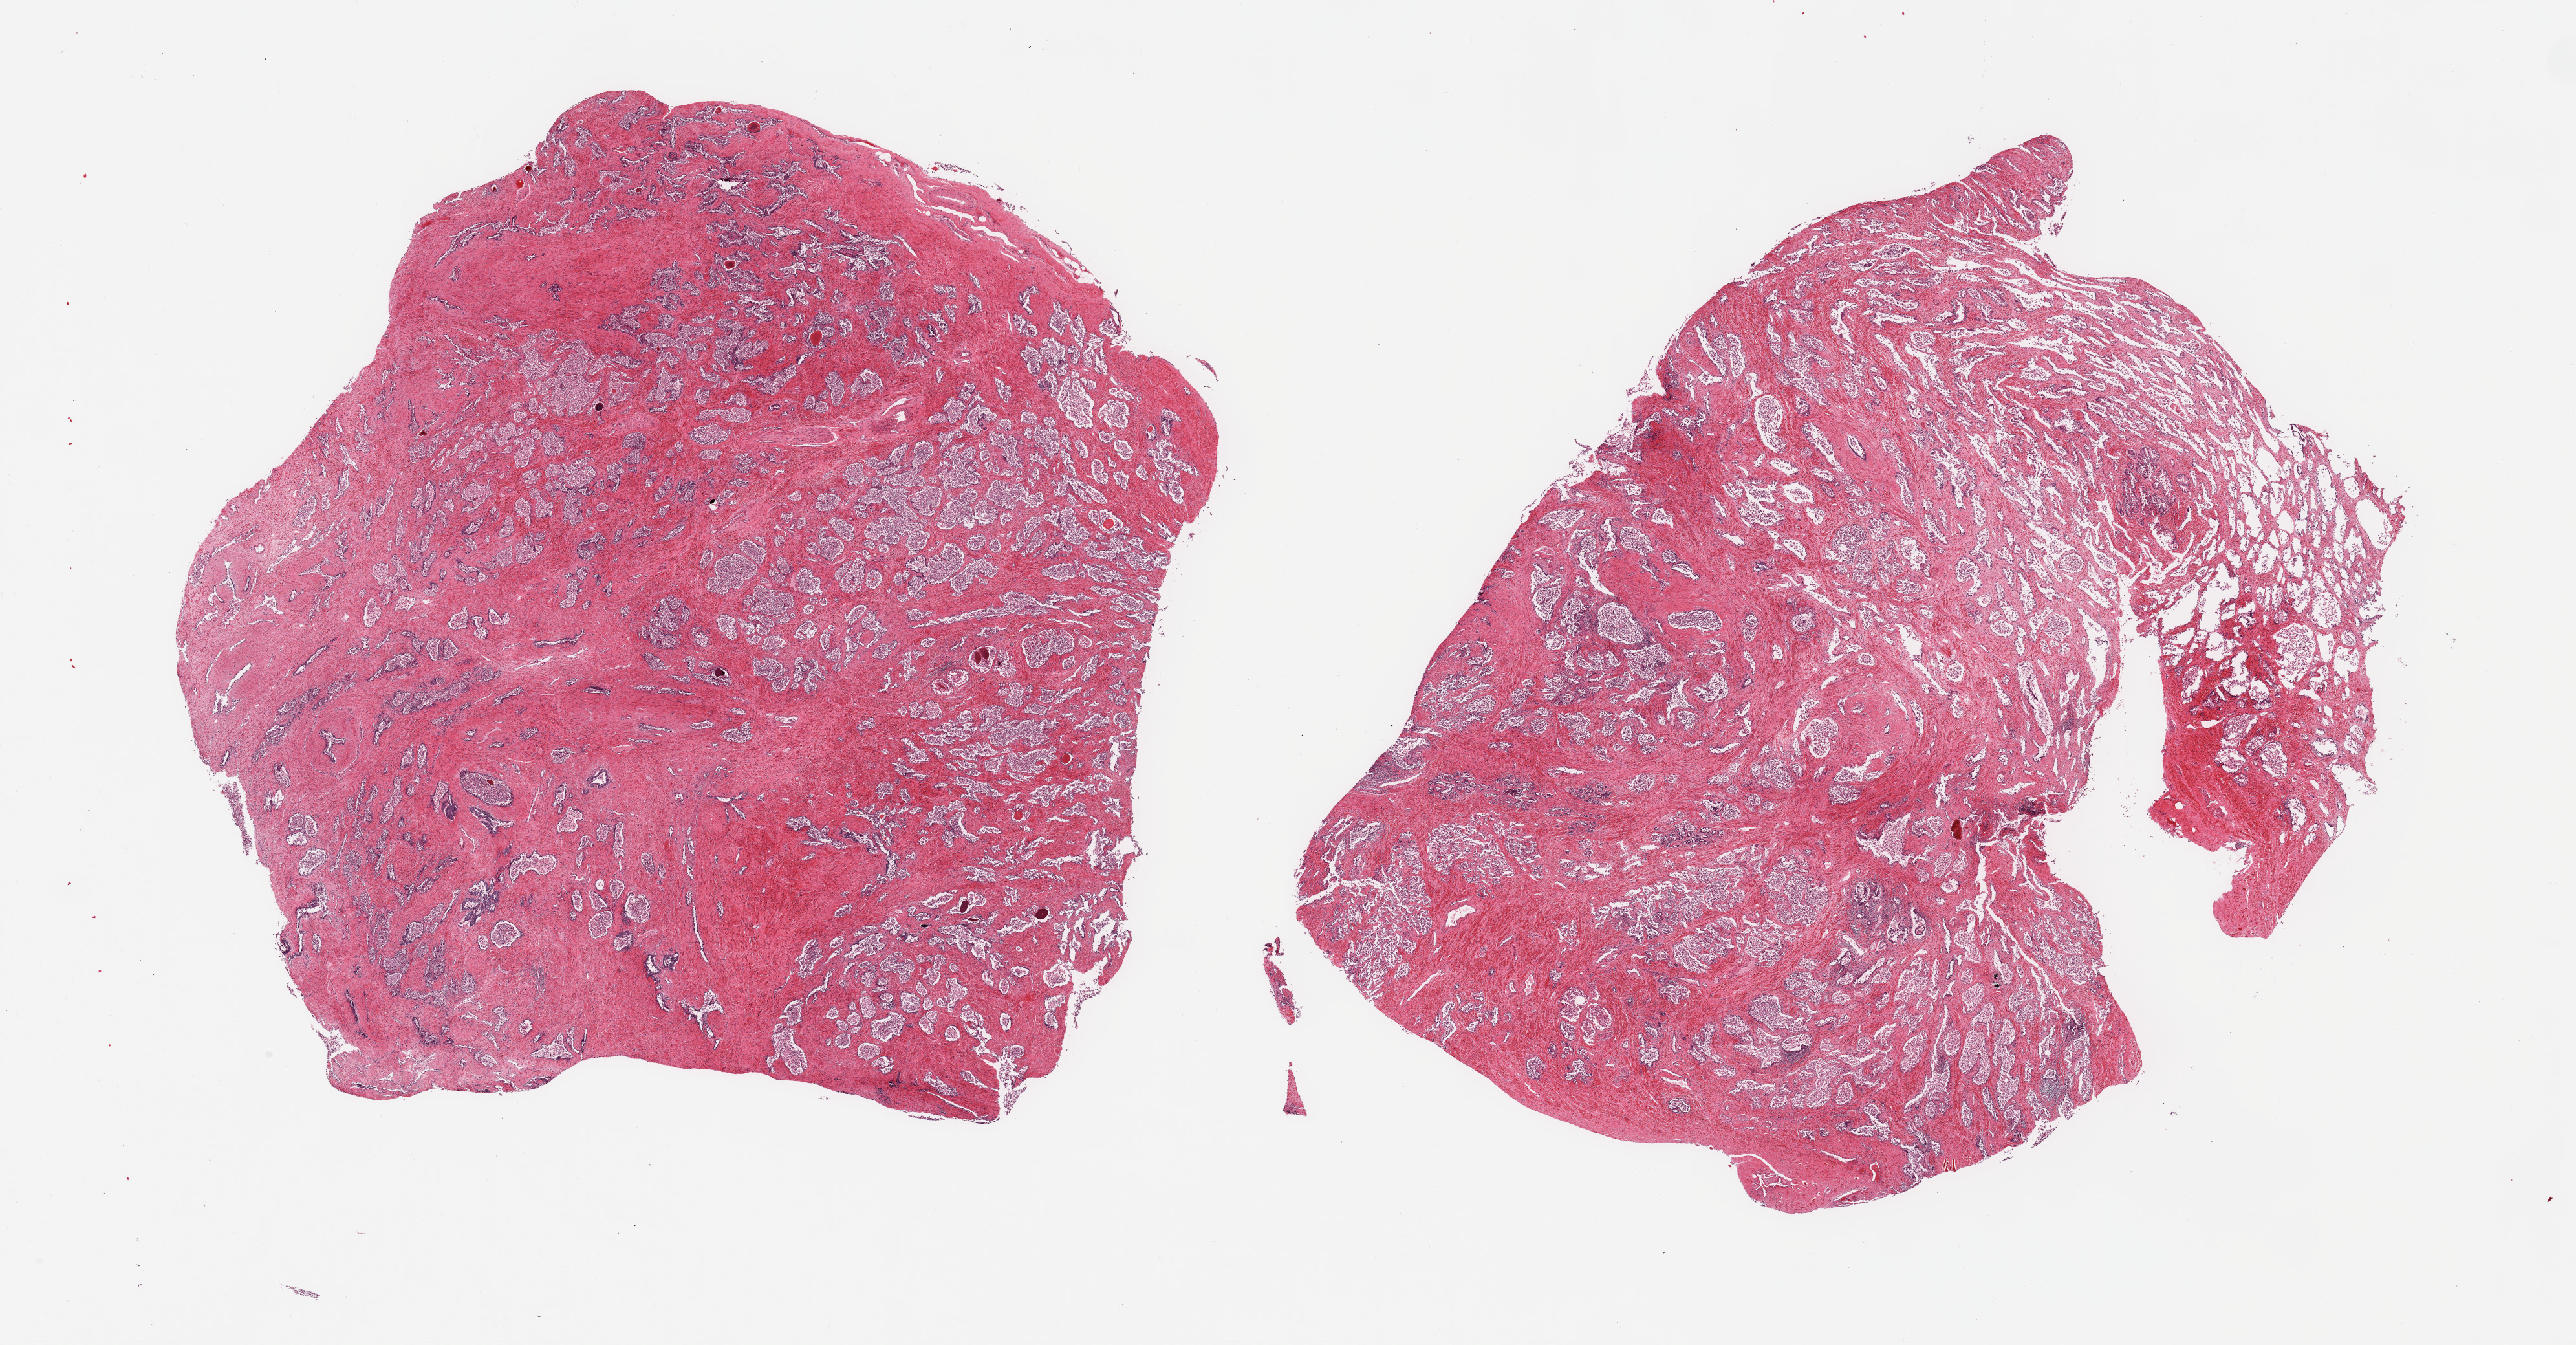
Digitized haematoxylin and eosin-stained section, whole scanned area (about 31.5 x 16.4 mm) shown as a low-resolution overview; PAXgene-fixed, paraffin-embedded tissue; section of prostate (target tissue); tissue donor sample. Male donor.
Reviewer comment on this tissue sample: 2 pieces, hyperplastic glandular pattern with advanced mucosal autolysis.